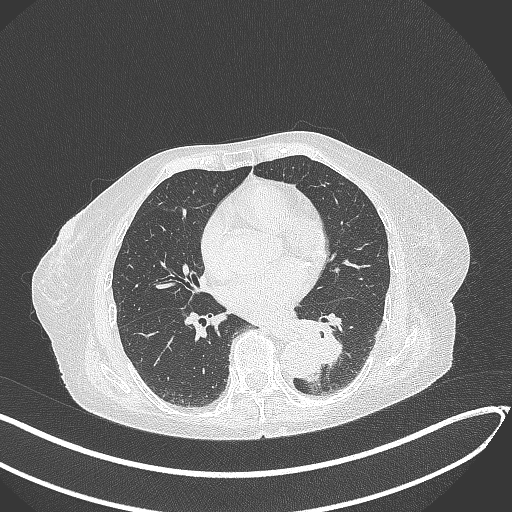
Chest CT, one axial slice; position 112 of 324 along the scan axis; reconstruction kernel B70f; lung window (W 1500 / L -600 HU); 1 mm slice thickness; 512 × 512 image matrix. Female patient, age 82 years. From the clinical record (not read from this slice): clinical TNM (as recorded): T1b N0 M1.
Annotated regions visible in this slice (rectangle marked by the reading radiologist):
- lung tumour (recorded histology: adenocarcinoma): box from (x=294, y=314) to (x=352, y=368) px